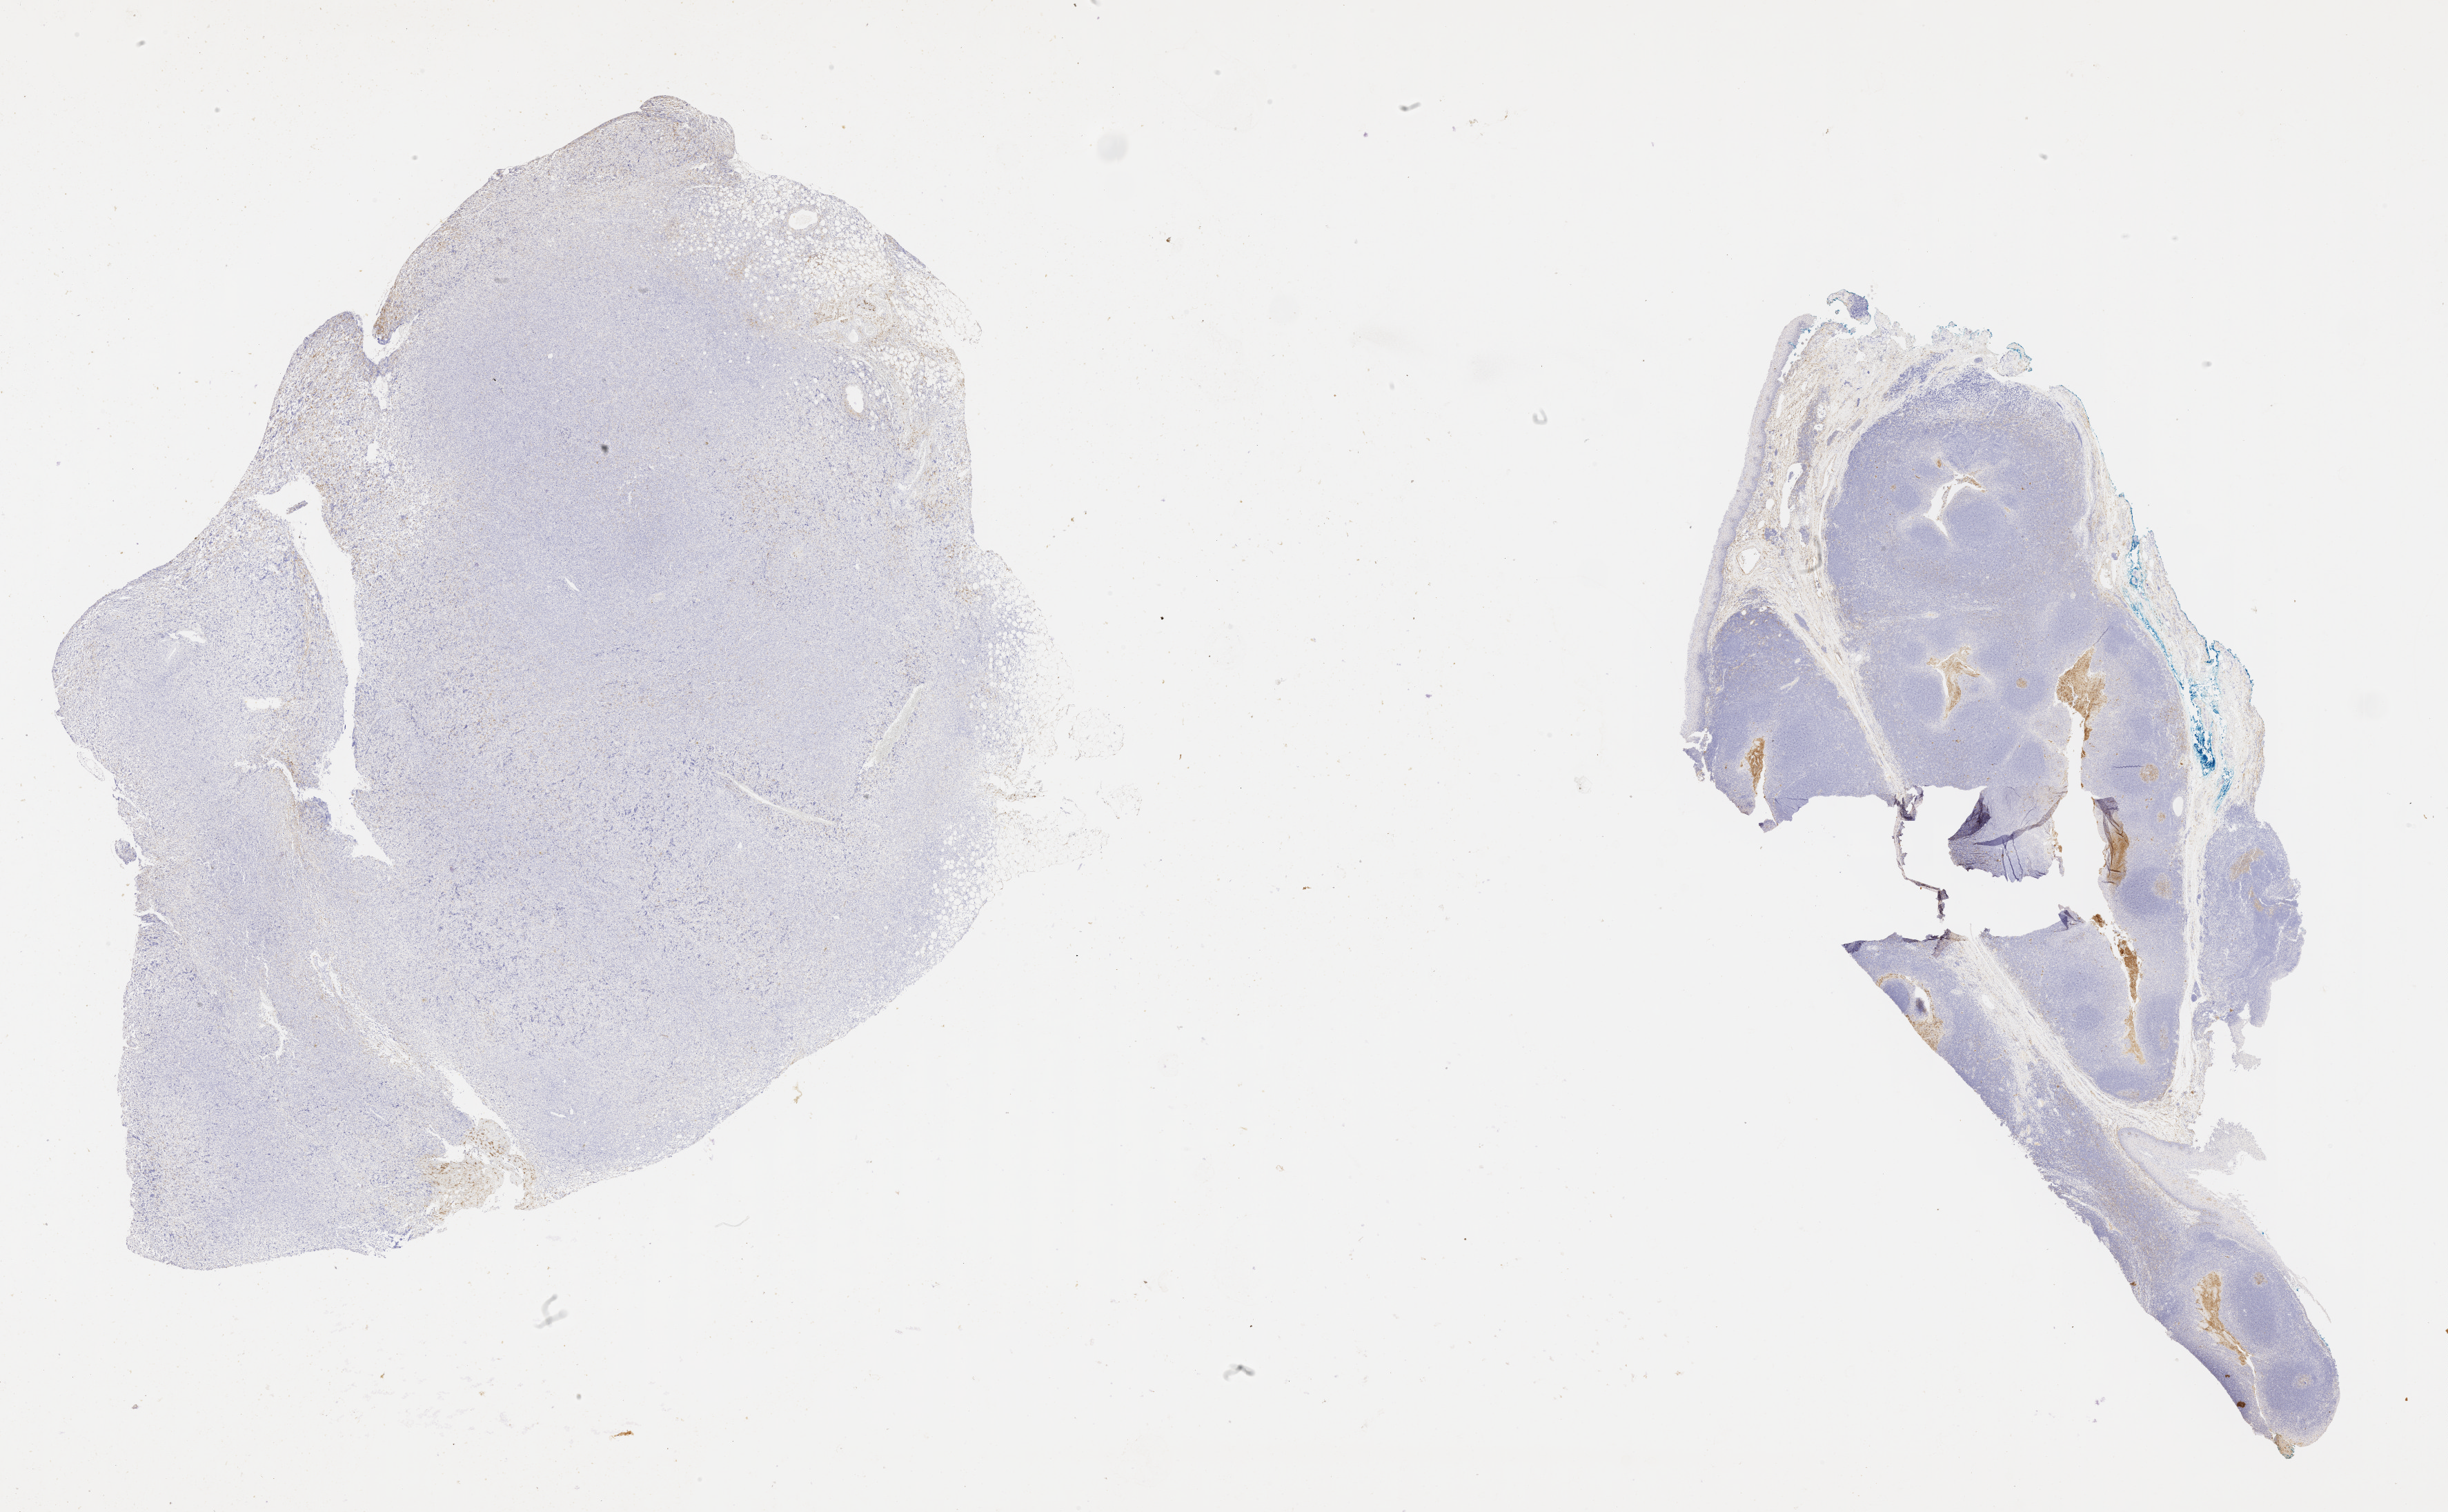
Immunohistochemistry (IHC) whole-slide image stained for CD10 — low-resolution overview of the scanned area, about 28.7 x 17.7 mm. Patient sex: female.
Specimen: tumor tissue.